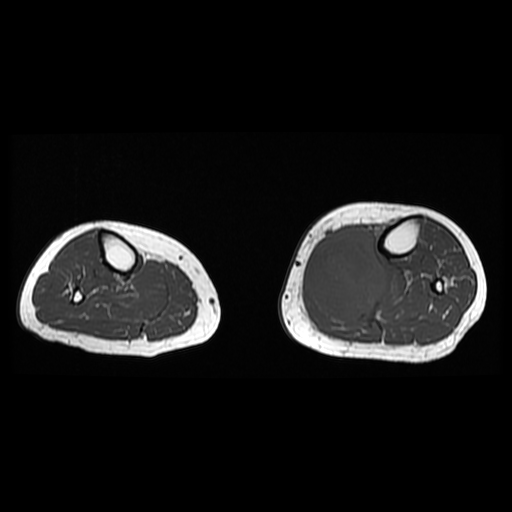
MRI of an extremity soft-tissue mass, one axial slice. 6 mm slice thickness. 512 × 512 image matrix. Female patient. From the clinical record (not read from this slice): histological type: extraskeletal high grade osteogenic sarcoma; grade: high; site of the primary tumour: left calf.
Annotated regions visible in this slice (manually delineated by an expert):
- gross tumour volume (mass): box from (x=308, y=226) to (x=387, y=321) px